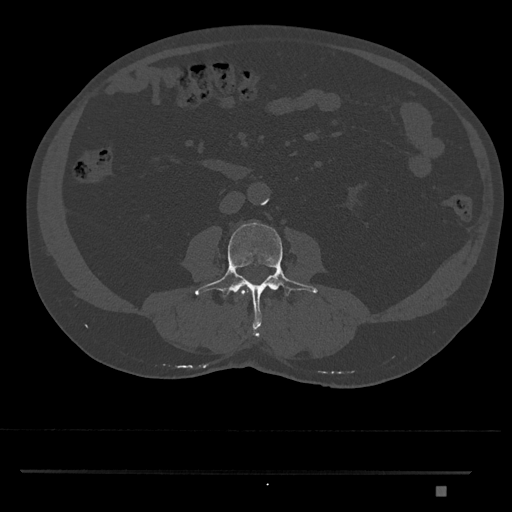
CT including the spine, one axial slice; position 684 of 1134 along the scan axis; reconstruction kernel Br40s/3; bone window (W 1800 / L 400 HU); 0.5 mm slice thickness; 512 × 512 image matrix, field of view 429 × 429 mm. Male patient, age 65 years. Case-level facts recorded for this patient, not image findings: primary cancer: prostate.
Structures marked on this image (semi-automatically segmented with operator editing):
- L2 vertebra: bounding box [x1, y1, x2, y2] px = [240, 289, 247, 296]
- L3 vertebra: [195, 222, 318, 337]